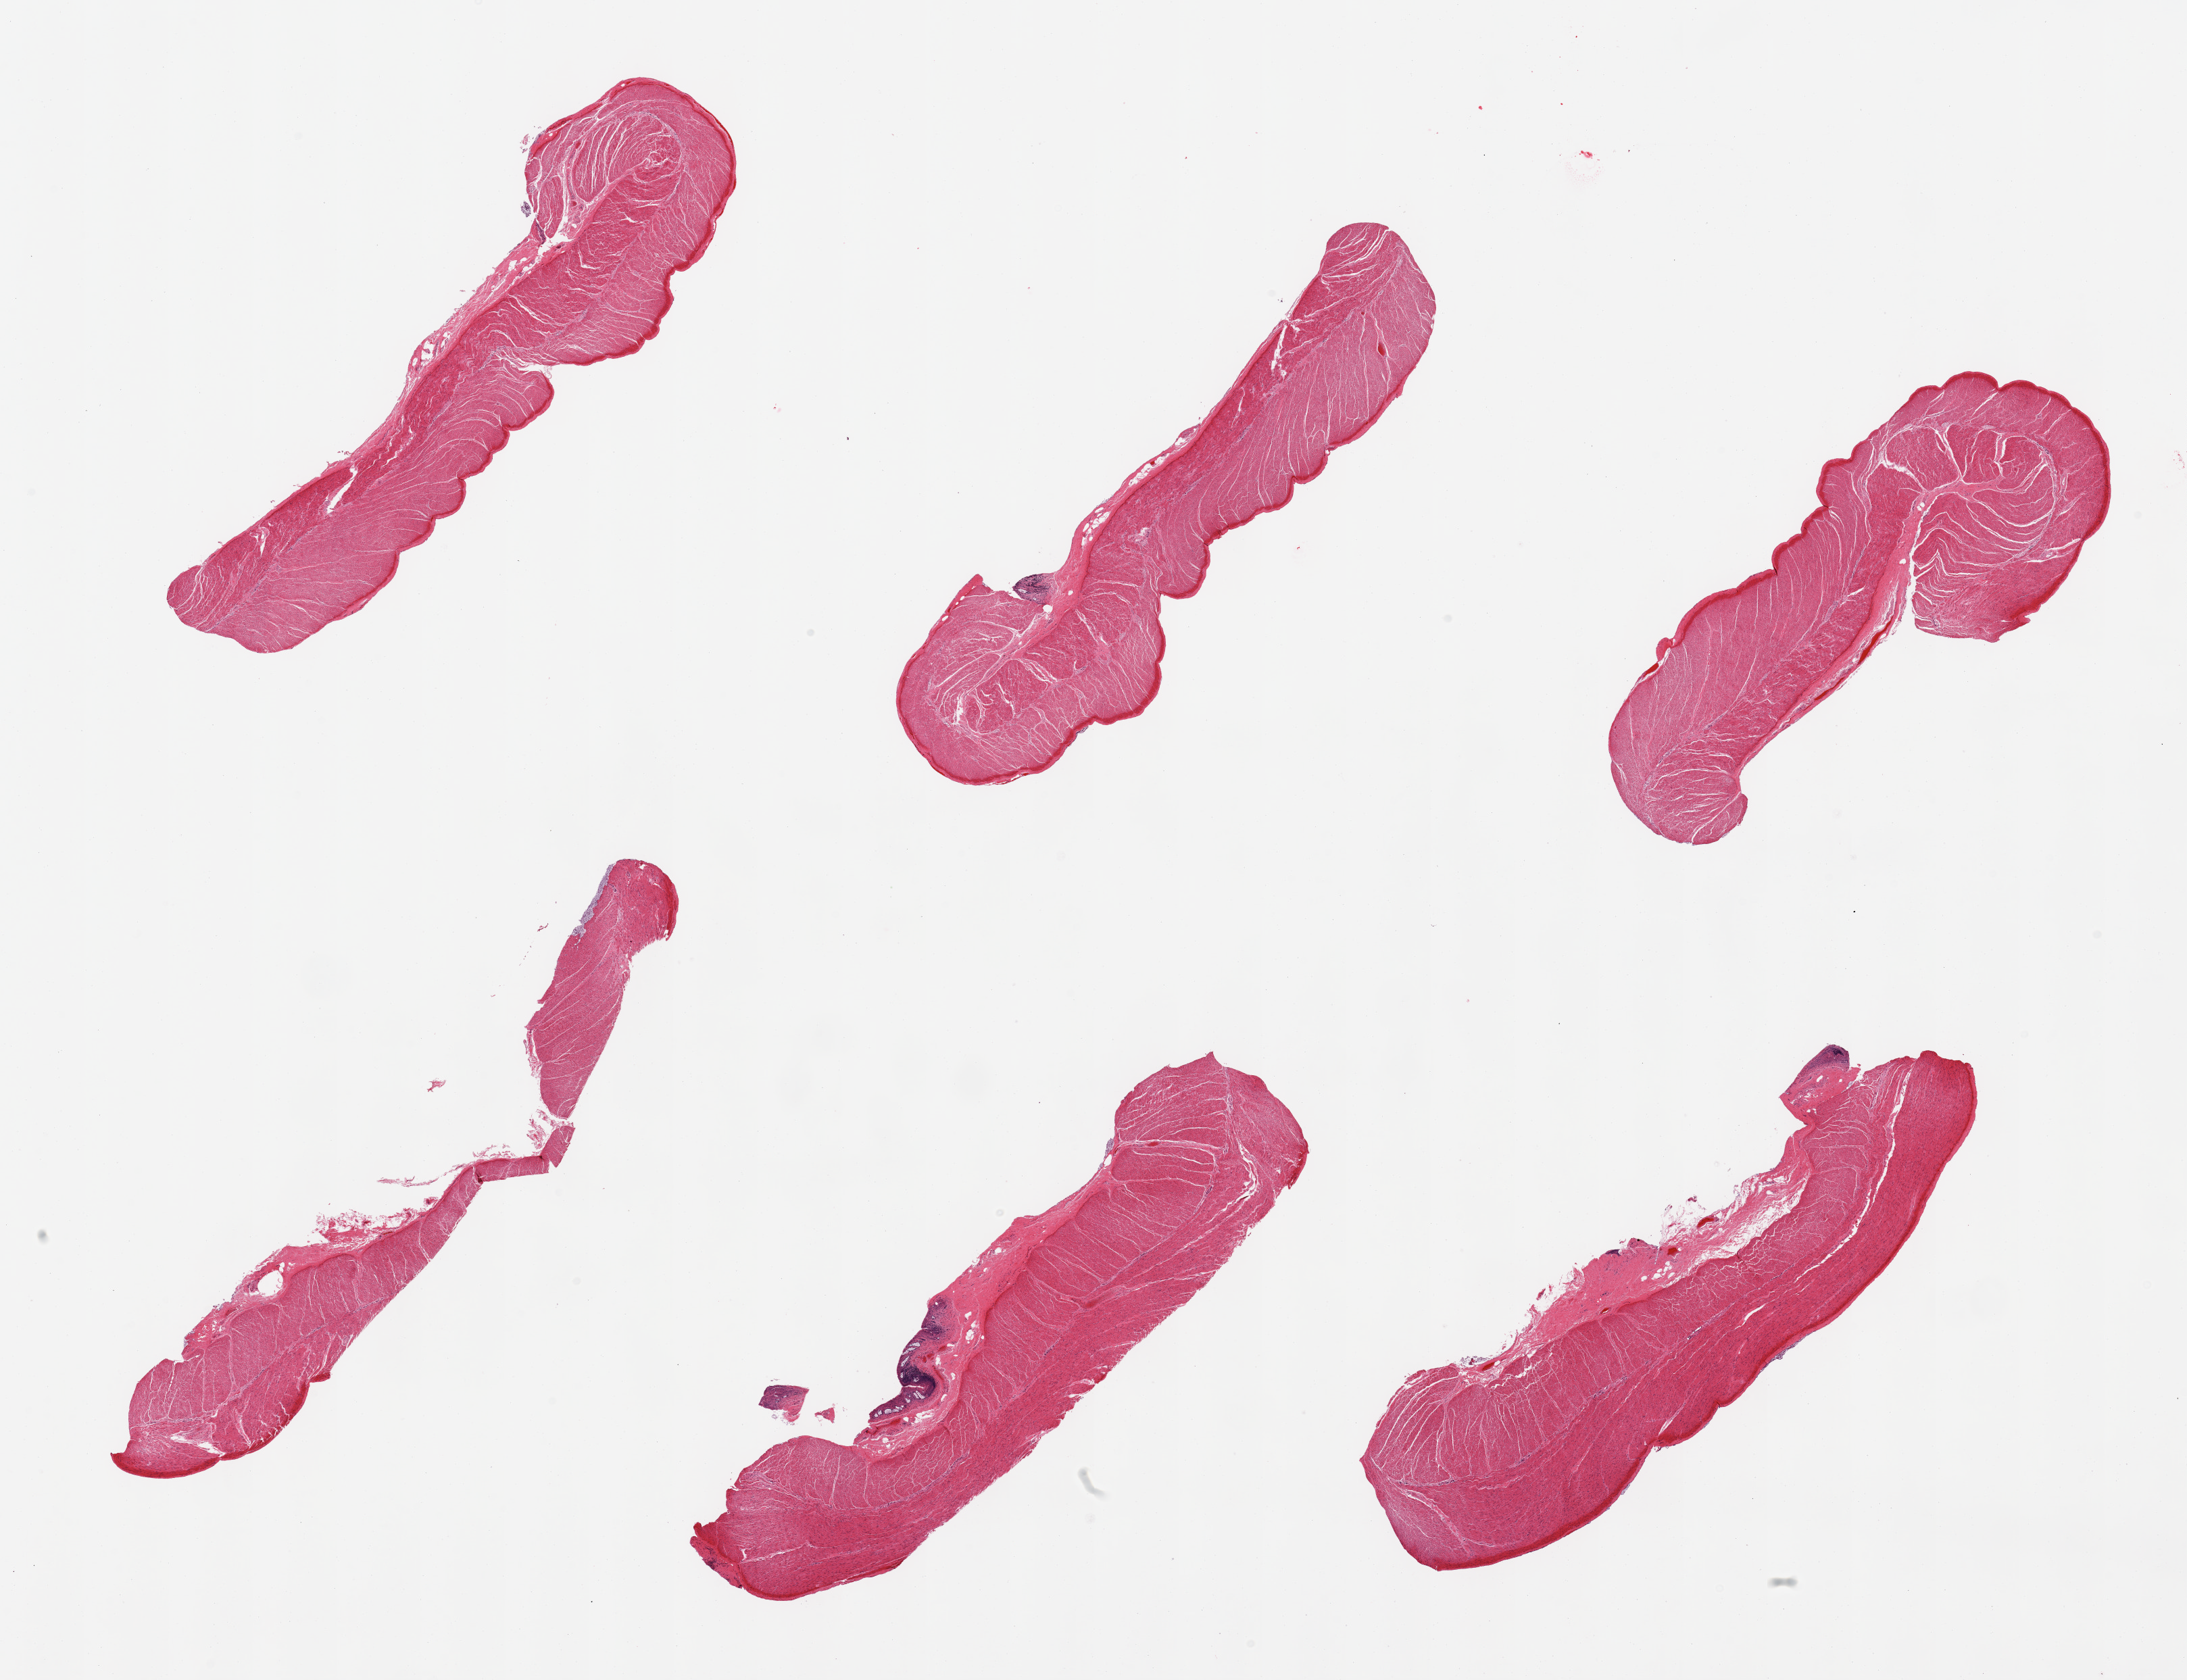
Digitized haematoxylin and eosin-stained section, low-resolution overview of the scanned area, about 25.6 x 19.7 mm; PAXgene-fixed paraffin-embedded (PFPE) section; sampled site (target tissue): sigmoid colon; donor tissue sample. Female donor.
- reviewer comment on this tissue sample: 6 pieces, target muscularis, minute trace autolyzed mucosa